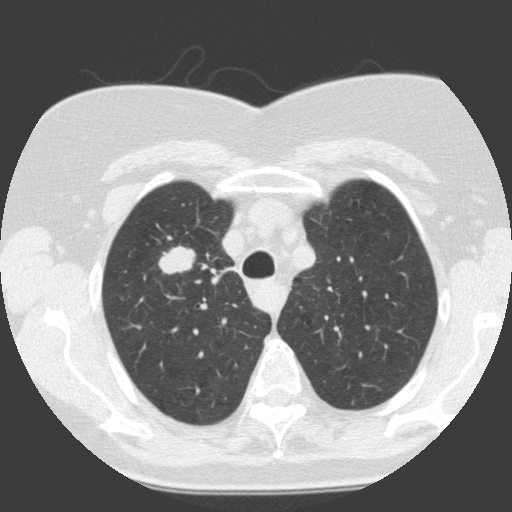
Low-dose screening chest CT, one axial slice; position 114 of 146 along the scan axis; 120 kVp; lung window (W 1500 / L -600 HU); 2 mm slice thickness; 512 × 512 image matrix, field of view 300 × 300 mm.
Outlined on this slice (manually delineated by an expert):
- lesion 1 (tumor, upper lobe of right lung): bounding box <158,245,196,275> (left, top, right, bottom; pixels)